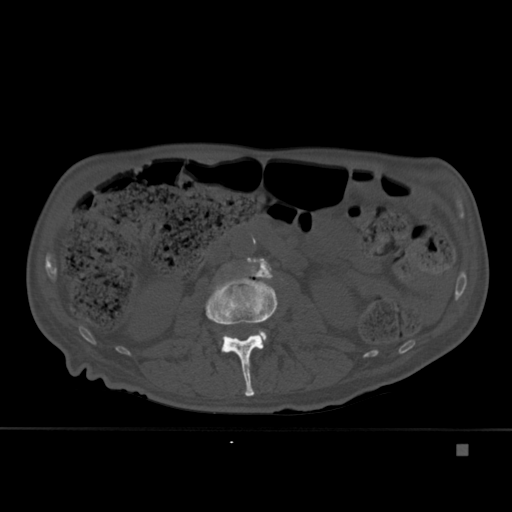
CT including the spine, one axial slice. Position 157 of 451 along the scan axis. Bone window (W 1800 / L 400 HU). 1.5 mm slice thickness. 512 × 512 image matrix, field of view 378 × 378 mm. Male patient, age 75 years. From the clinical record (not read from this slice): primary cancer: prostate.
Annotated regions visible in this slice (semi-automatic segmentation, software-assisted and operator-edited):
- L2 vertebra: bounding box <205,275,278,397> (left, top, right, bottom; pixels)
- L3 vertebra: <220,257,273,348>